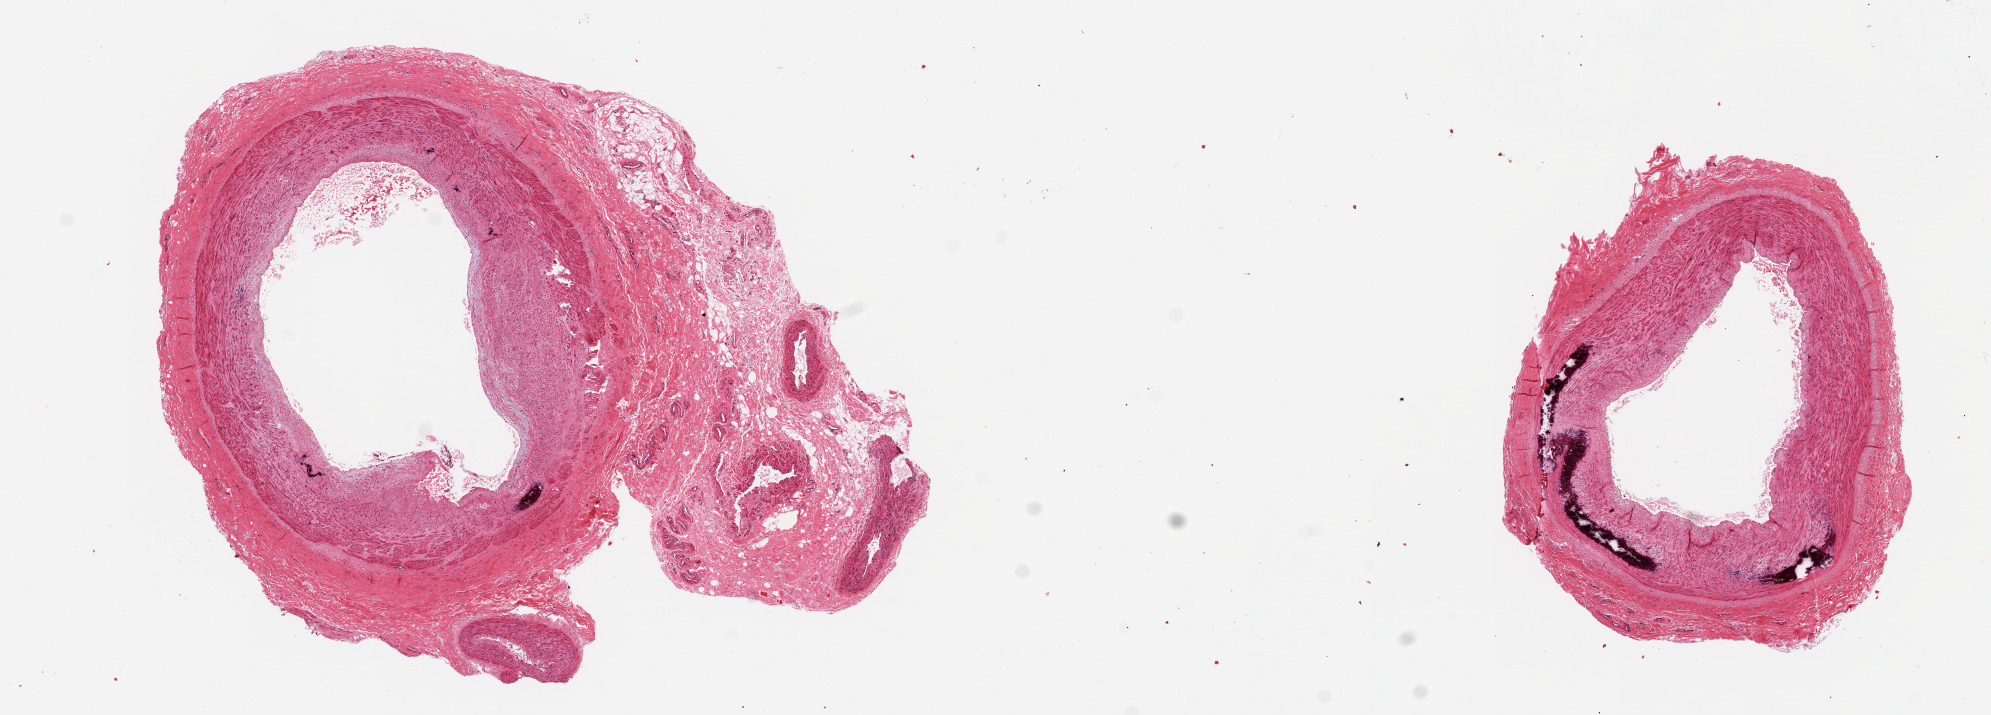
H&E whole-slide image — a low-resolution overview of the entire scanned area, about 15.8 x 5.7 mm; PAXgene-fixed, paraffin-embedded tissue; target tissue: tibial artery; donor tissue sample. Donor: male.
• reviewer comment on this tissue sample: 2 pieces ~4mm d, clean specimens, but one aliqout with adherent fibsrovascular nubbin ~4x2mm